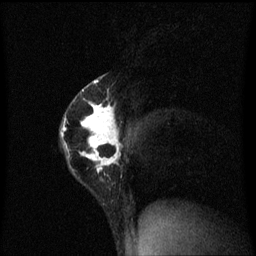
Breast MRI (dynamic contrast-enhanced), one sagittal slice. Position 40 of 60 along the scan axis. Dynamic contrast-enhanced series, image 2 of 3 at this slice position (ordered by acquisition). 1.5 T. TE 4.2 ms, TR 8.4 ms. 256 × 256 image matrix. Female patient, age 40 years.
Annotated regions visible in this slice (semi-automatically segmented with operator editing):
- analysis volume of interest (the breast-tissue region the enhancement analysis was run in; not a lesion): bounding box <61,74,124,187> (left, top, right, bottom; pixels)
- tumour enhancement mask (voxels above the 70 % enhancement threshold inside the analysis volume of interest): <61,80,123,173>